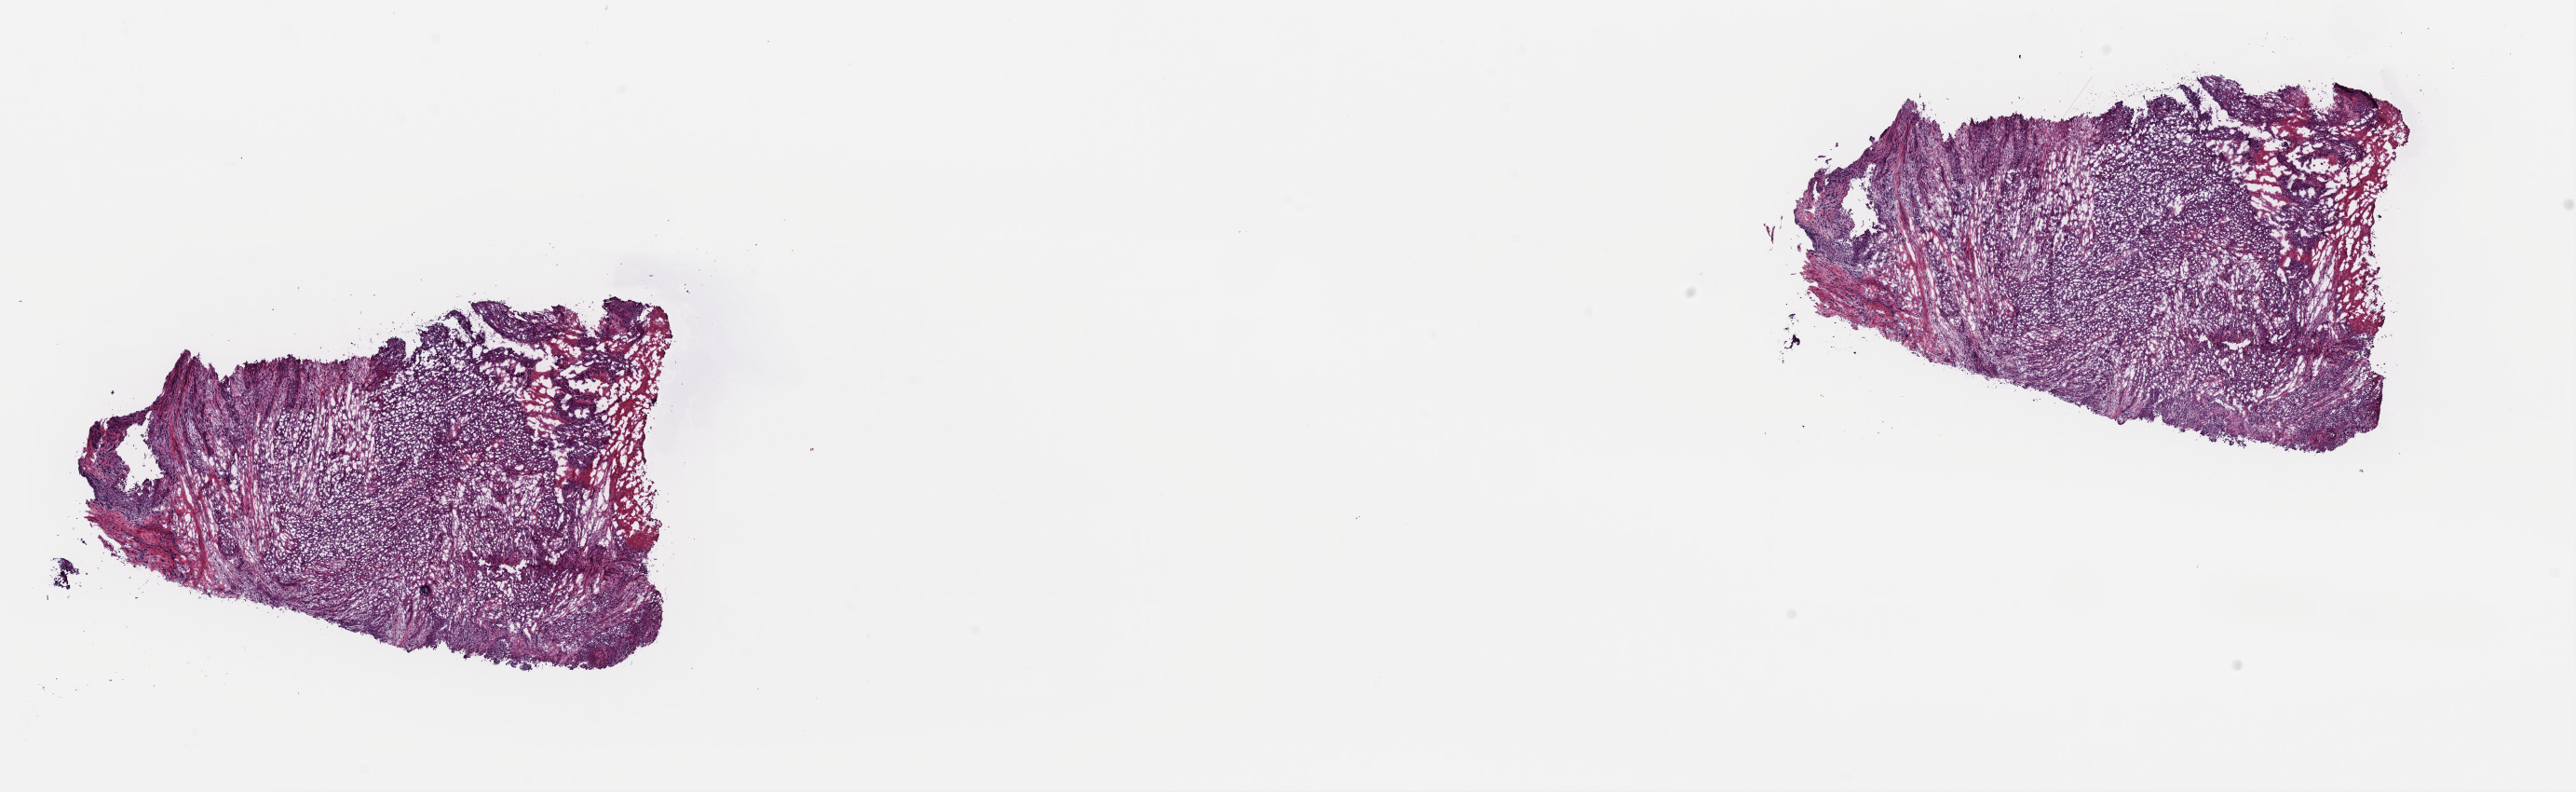
H&E whole-slide image — low-resolution overview of the scanned area, about 21.9 x 6.7 mm (acquisition: 40x scan); frozen section from the top of the tissue portion; primary tumour sample from the cervix. Female, age 49 years at initial diagnosis. Histologic grade: G4 (undifferentiated). Composition of this section per pathologist review: tumour cells 95%, tumour nuclei 95%, normal cells 0%, stromal cells 0%, necrosis 5%. Infiltration values recorded for this section: lymphocyte infiltration 1%, monocyte infiltration 1%, neutrophil infiltration 0%.
FIGO stage: IIA1. Diagnosis: Squamous cell carcinoma, NOS. Lymph nodes positive (case pathology): 0 of 40 examined.